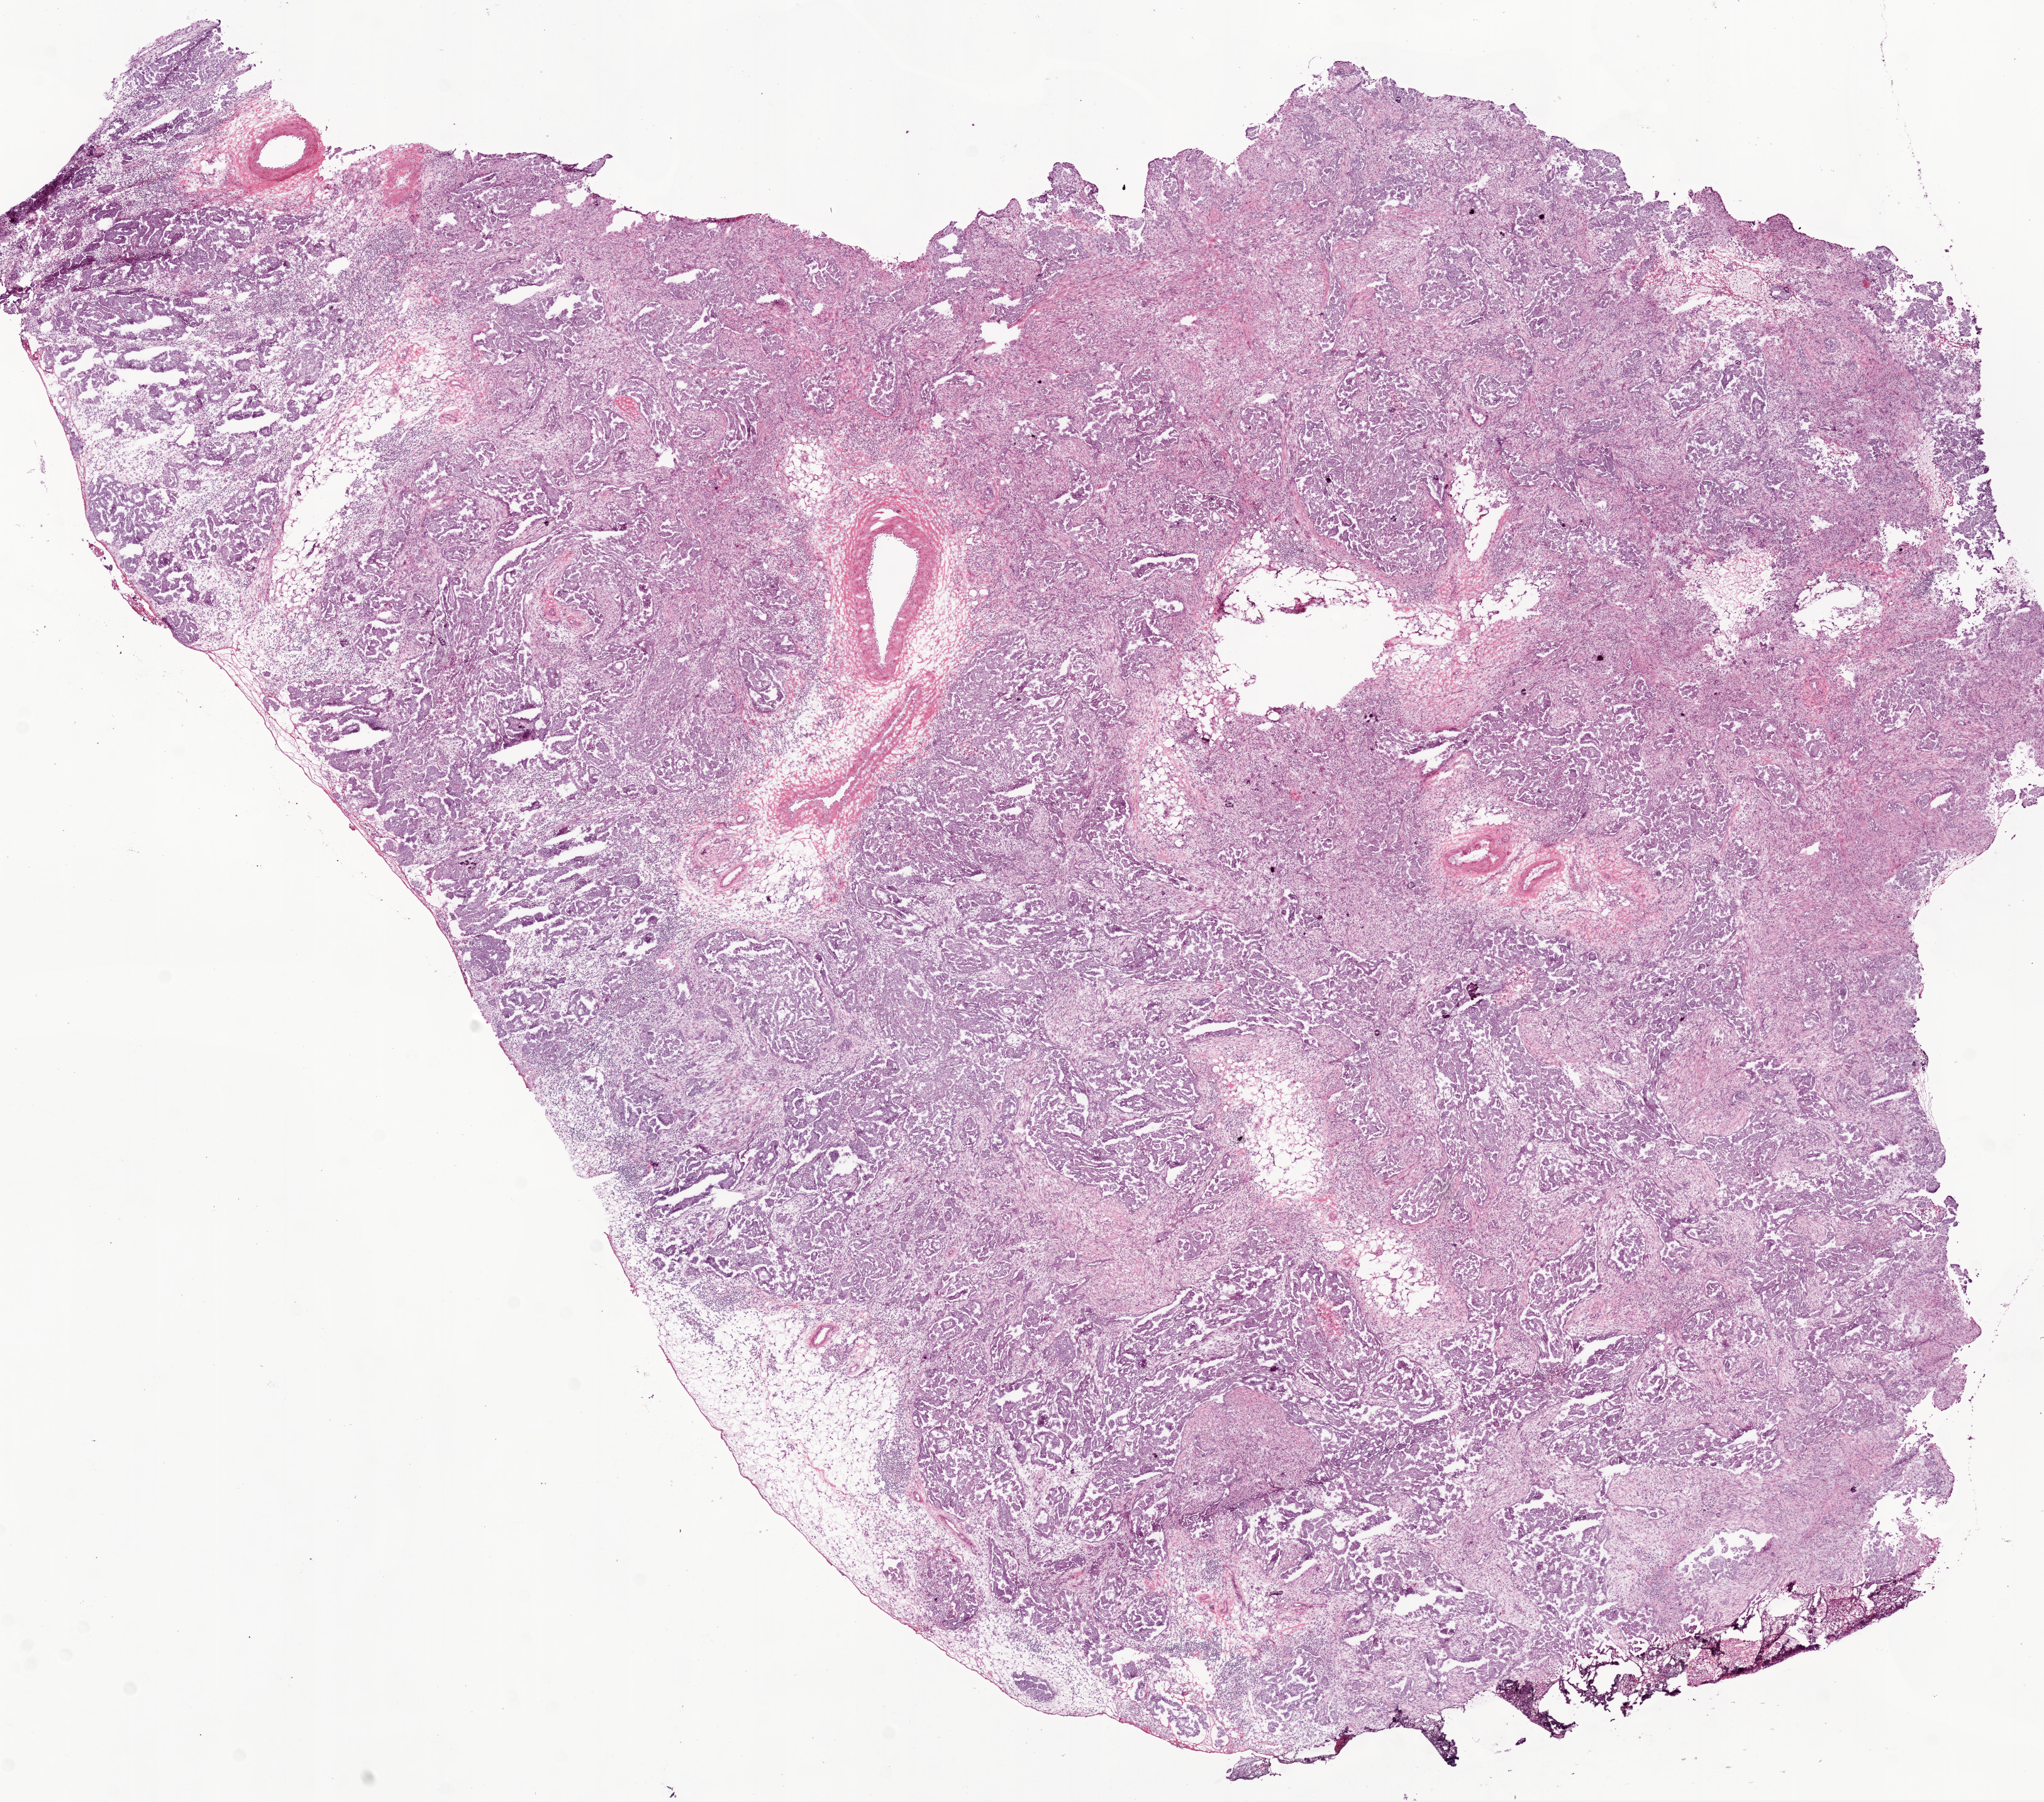
H&E-stained whole-slide image — shown as a low-resolution overview of the whole scanned area (about 13.0 x 11.5 mm); frozen section from the bottom of the tissue portion; primary tumour sample from the ovary. Female patient; age at initial diagnosis 64 years. Histologic grade: G3 (poorly differentiated). Pathologist review of this section (percent, as recorded): tumour cells 79%, tumour nuclei 80%, normal cells 0%, stromal cells 20%, necrosis 1%.
- histologic diagnosis: Serous cystadenocarcinoma, NOS
- FIGO stage: IIIC